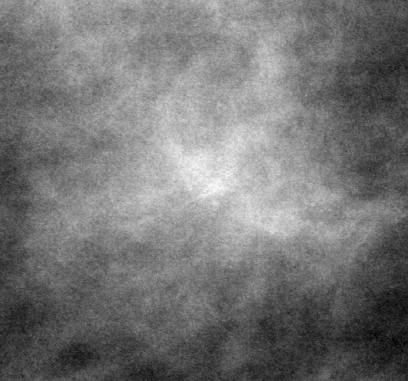
Cropped region of a digitized screen-film mammogram centred on a radiologist-marked abnormality, left breast, CC view.
Marked abnormality: mass, shape focal asymmetric density; BI-RADS assessment category 3; subtlety rating 4 on a 1 (subtle) to 5 (obvious) scale; benign; no additional work-up was recommended (benign without callback).